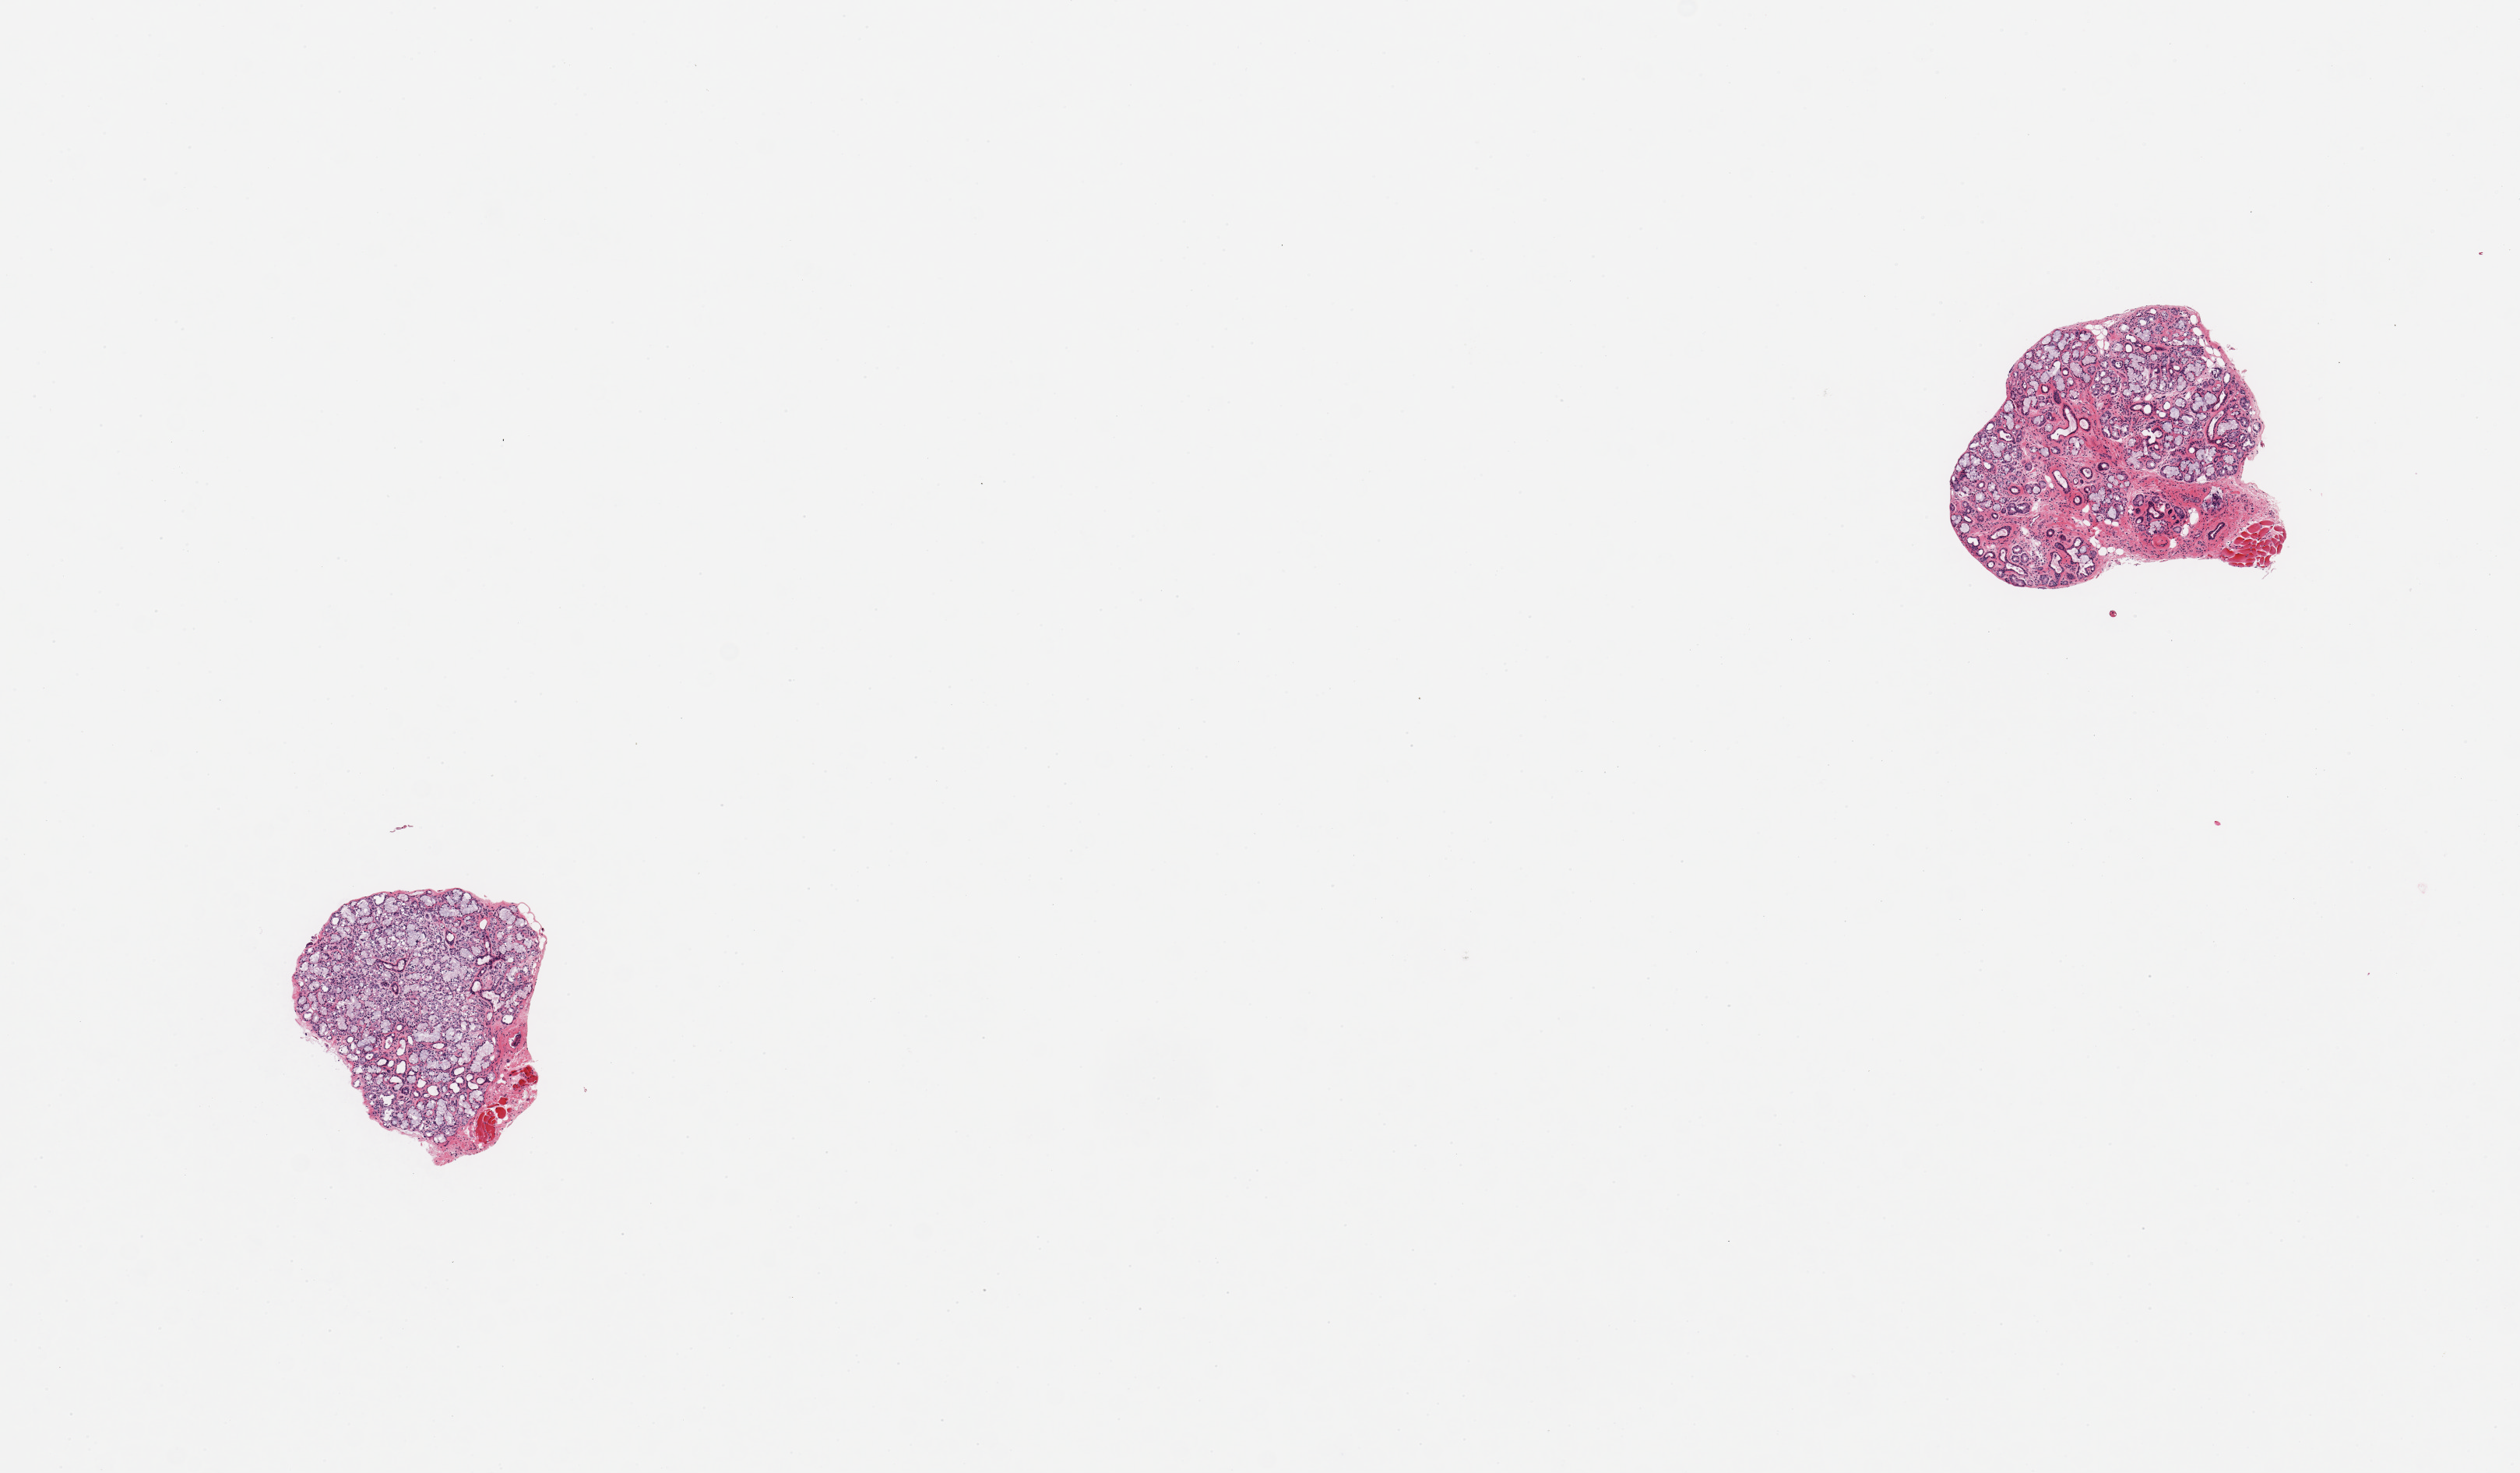
Digitized H&E-stained section — shown as a low-resolution overview of the whole scanned area (about 12.8 x 7.5 mm); PAXgene-fixed paraffin-embedded (PFPE) section; target tissue: minor salivary gland; tissue donor sample.
- reviewer comment on this tissue sample: 2 pieces; well dissected glands with 5% skeletal muscle on edge